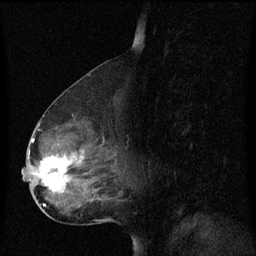
Breast MRI (dynamic contrast-enhanced), one sagittal slice. Slice 36 of 60 in the series (ordered by position). Dynamic contrast-enhanced series, image 2 of 3 at this slice position (ordered by acquisition). 1.5 T. TE 4.2 ms, TR 8.4 ms. 2 mm slice thickness. 256 × 256 image matrix. Patient: female, 49 years. From the clinical record (not read from this slice): setting: breast cancer imaged before/during neoadjuvant chemotherapy; receptor status: HR-positive, HER2-negative.
Structures marked on this image (semi-automatic segmentation, software-assisted and operator-edited):
- analysis volume of interest (the breast-tissue region the enhancement analysis was run in; not a lesion): bounding box [x1, y1, x2, y2] px = [22, 126, 117, 201]
- tumour enhancement mask (voxels above the 70 % enhancement threshold inside the analysis volume of interest): [32, 140, 85, 193]